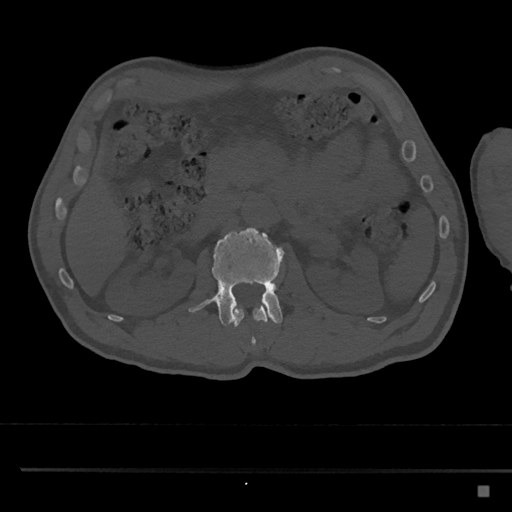
CT including the spine, one axial slice; position 783 of 797 along the scan axis; reconstruction kernel Br40s/3; bone window (W 1800 / L 400 HU); 0.5 mm slice thickness; 512 × 512 image matrix. Patient: male, 59 years. From the clinical record (not read from this slice): primary cancer: prostate.
Annotated regions visible in this slice (semi-automatic segmentation, software-assisted and operator-edited):
- L1 vertebra: bounding box <233,305,269,345> (left, top, right, bottom; pixels)
- L2 vertebra: <188,228,284,327>